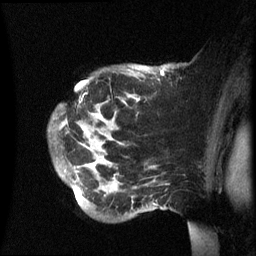
Breast MRI (dynamic contrast-enhanced), one sagittal slice. Slice 46 of 60 in the series (ordered by position). Dynamic contrast-enhanced series, image 2 of 3 at this slice position (ordered by acquisition). 1.5 T. TE 4.2 ms, TR 8.4 ms. 256 × 256 image matrix, field of view 230 × 230 mm. Patient: female, 49 years.
Annotated regions visible in this slice (semi-automatically segmented with operator editing):
- analysis volume of interest (the breast-tissue region the enhancement analysis was run in; not a lesion): bounding box (x1, y1, x2, y2) in pixels: (49, 64, 173, 220)
- tumour enhancement mask (voxels above the 70 % enhancement threshold inside the analysis volume of interest): (66, 70, 164, 193)